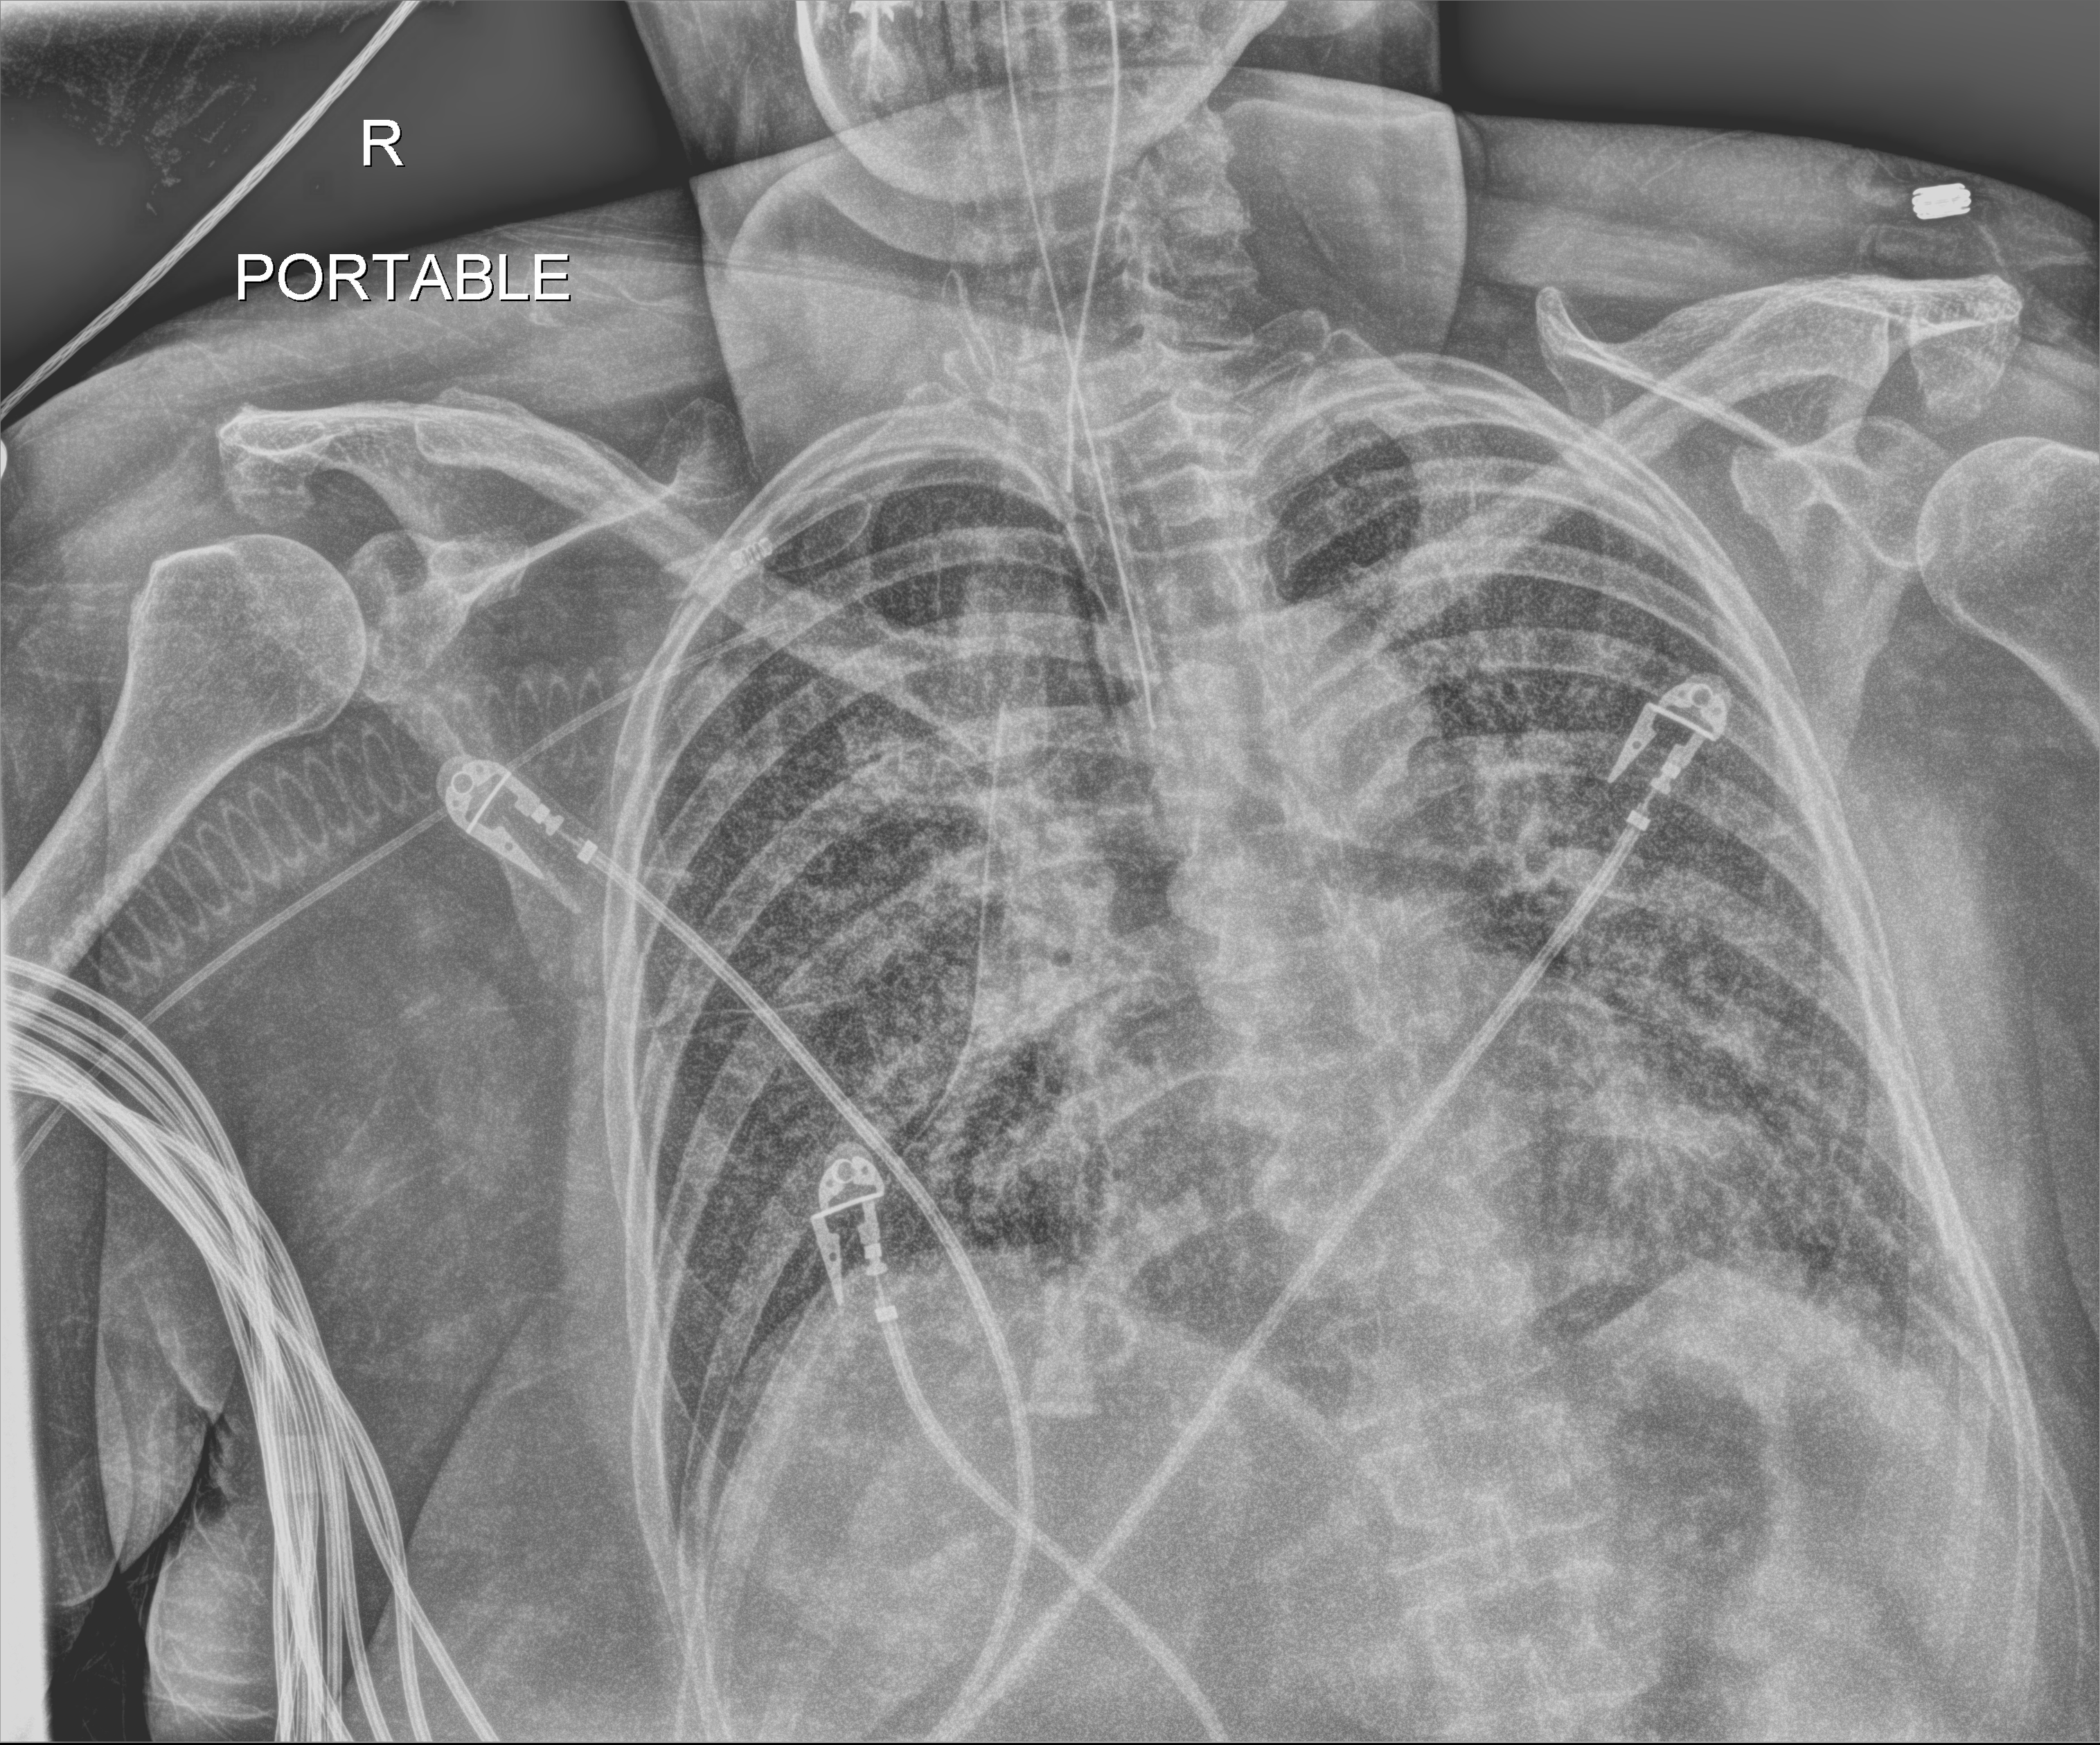
Bedside chest radiograph (digital radiography); anteroposterior (AP) projection. Patient hospitalised with COVID-19; female, aged 60–74 years.
Admission-level facts for this patient (not findings on this image; timing relative to this image not recorded):
- length of hospital stay: 38 days